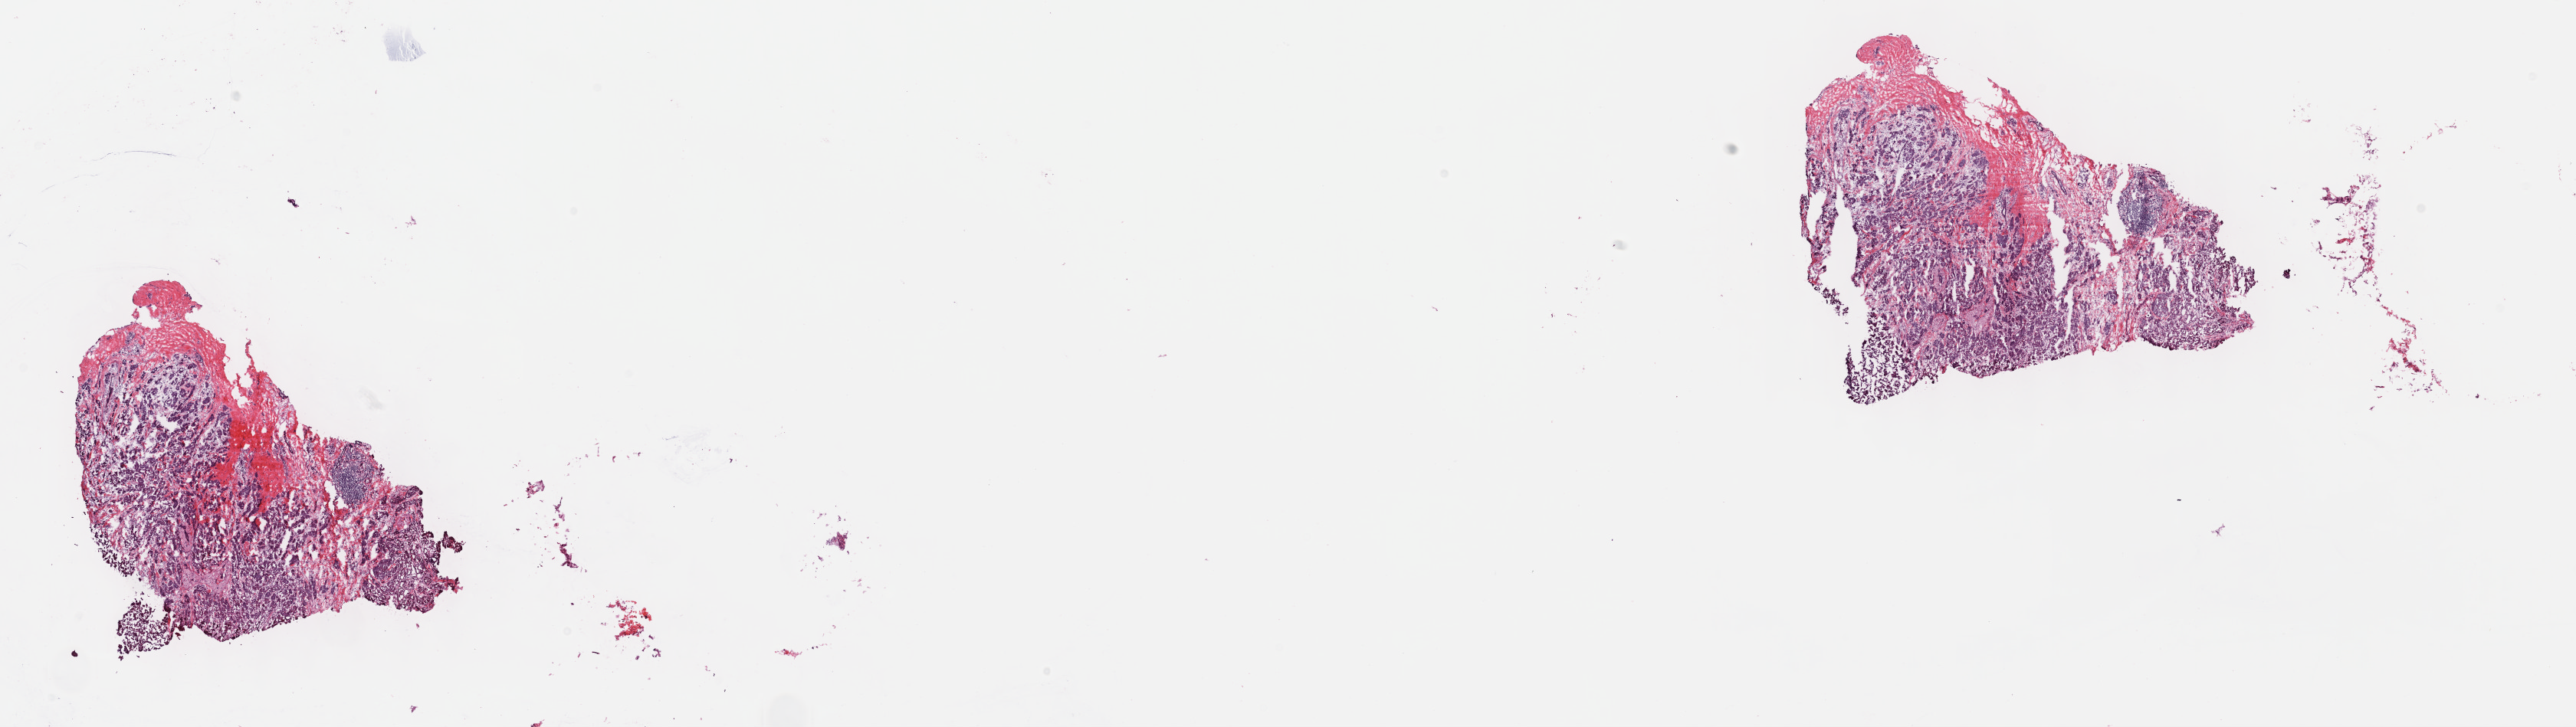
Digitized H&E tissue section (whole slide) — whole scanned area (about 27.2 x 7.7 mm) shown as a low-resolution overview, frozen section from the top of the tissue portion, sample: primary tumour, breast. Female patient; age at initial diagnosis 75 years. Composition of this section per pathologist review: tumour cells 70%, tumour nuclei 70%, normal cells 8%, stromal cells 20%, necrosis 2%. Infiltration values recorded for this section: lymphocyte infiltration 4%, monocyte infiltration 0%, neutrophil infiltration 0%.
AJCC pathologic stage: IIIA (6th edition). Laterality: right. Lymph nodes positive (case pathology): 5 of 18 examined. Diagnosis: Infiltrating duct carcinoma, NOS.